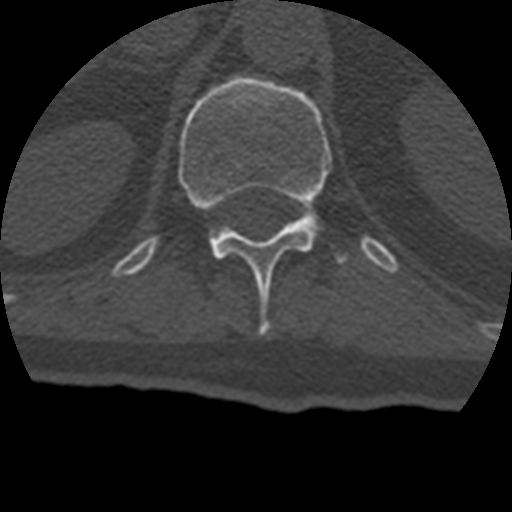
CT including the spine, one axial slice. Slice 169 of 399 in the series (ordered by position). Reconstruction kernel STANDARD. 120 kVp. Bone window (W 1800 / L 400 HU). 1.25 mm slice thickness. 512 × 512 image matrix, field of view 160 × 160 mm. Patient age 69 years. From the clinical record (not read from this slice): primary cancer: prostate.
Structures marked on this image (semi-automatic segmentation, software-assisted and operator-edited):
- T12 vertebra: bounding box <178,76,332,335> (left, top, right, bottom; pixels)